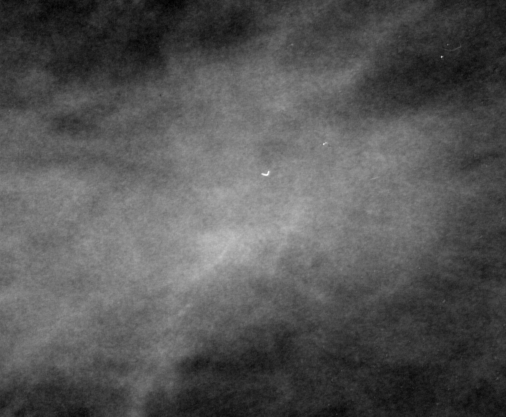
Crop from a digitized film mammogram around one marked abnormality; left breast; CC view; BI-RADS breast density category 2 (scale 1–4).
- Mass, shape irregular, margins spiculated; BI-RADS assessment category 5; subtlety rating 5 on a 1 (subtle) to 5 (obvious) scale; pathology result (as recorded, not read from the image): malignant.